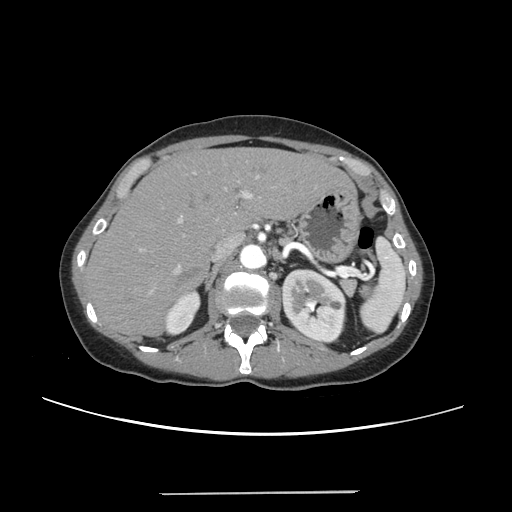
Contrast-enhanced abdominal CT, one axial slice; position 163 of 240 along the scan axis; 120 kVp; intravenous contrast given; soft-tissue window (W 400 / L 40 HU); 1.25 mm slice thickness; 512 × 512 image matrix, field of view 371 × 371 mm. Female patient, age 60 years. Case-level facts recorded for this patient, not image findings: diagnosis: colorectal cancer liver metastases, imaged before liver resection; multiple liver metastases: no; largest metastasis: 1.5 cm; disease in both lobes: no.
Annotated regions visible in this slice (expert manual segmentation):
- liver: box from (x=87, y=147) to (x=348, y=335) px
- planned liver remnant (the part of the liver to remain after resection): (x=87, y=147)–(x=347, y=334)
- portal vein (with intrahepatic branches): (x=139, y=172)–(x=259, y=293)